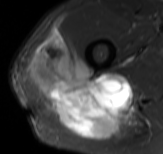
MRI of an extremity soft-tissue mass, one axial slice; slice 57 of 61 in the series (ordered by position); STIR; MR volume resampled by the dataset authors to the PET/CT grid (not the native acquisition matrix); 163 × 154 image matrix. Male patient. Case-level facts recorded for this patient, not image findings: histological type: poorly differentiated synovial sarcoma; grade: high; site of the primary tumour: right buttock.
Outlined on this slice (expert contour drawn on MRI and transferred to this co-registered scan by the dataset authors):
- gross tumour volume including surrounding oedema: bounding box [x1, y1, x2, y2] px = [25, 30, 145, 140]
- gross tumour volume (mass): [27, 30, 133, 140]